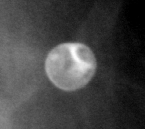
Region of interest cut from a scanned film mammogram (one marked finding); left breast; CC view.
Marked abnormality: calcifications, morphology lucent center; BI-RADS assessment category 2; subtlety rating 5 on a 1 (subtle) to 5 (obvious) scale; benign without callback (not worked up further).